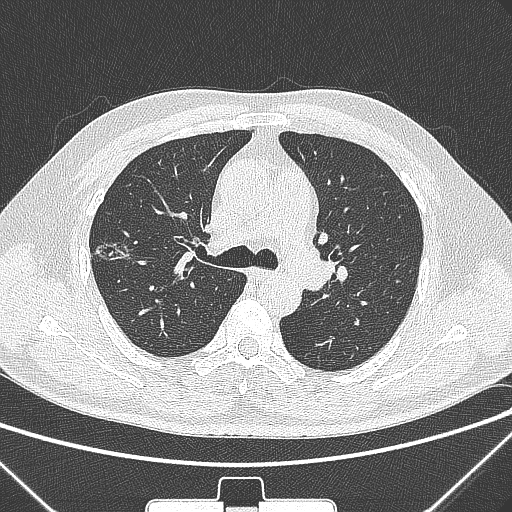
Chest CT, one axial slice. Slice 200 of 320 in the series (ordered by position). 120 kVp. Lung window (W 1500 / L -600 HU). 512 × 512 image matrix. Male patient, age 58 years. From the clinical record (not read from this slice): clinical TNM (as recorded): T1c N0 M0; histopathological grade: G2.
Structures marked on this image (bounding box drawn by a radiologist):
- lung tumour (recorded histology: adenocarcinoma): bounding box (x1, y1, x2, y2) in pixels: (87, 236, 139, 284)